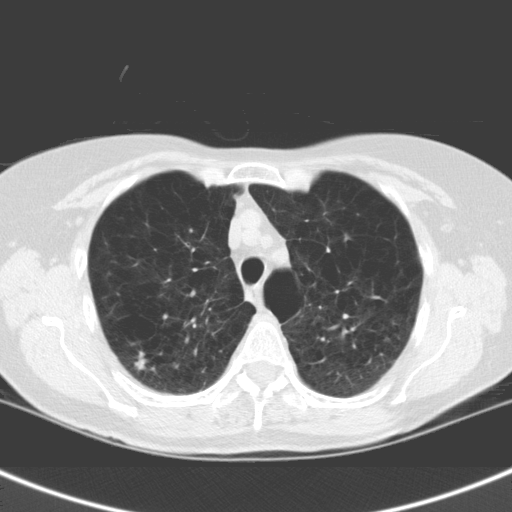
Low-dose screening chest CT, axial slice; second annual screen; lung window (W 1500 / L -600 HU); 3.2 mm slice thickness. Female participant, aged 63 years at enrolment. Current smoker at enrolment.
Lesion marked by an expert reader, bounding box [x1, y1, x2, y2] px = [114, 339, 161, 387]. Screening reader's record for this exam (one nodule recorded; not confirmed to be the boxed lesion): non-calcified nodule or mass ≥4 mm, right upper lobe, 7 × 7 mm, spiculated (stellate) margins, soft tissue attenuation, pre-existing on the prior screen: no. Official screen result: positive, other. Lung cancer was diagnosed 228 days after this screen: squamous cell carcinoma, NOS, right upper lobe, moderately differentiated (G2), stage IA (AJCC 6th edition), 14 mm at pathology.